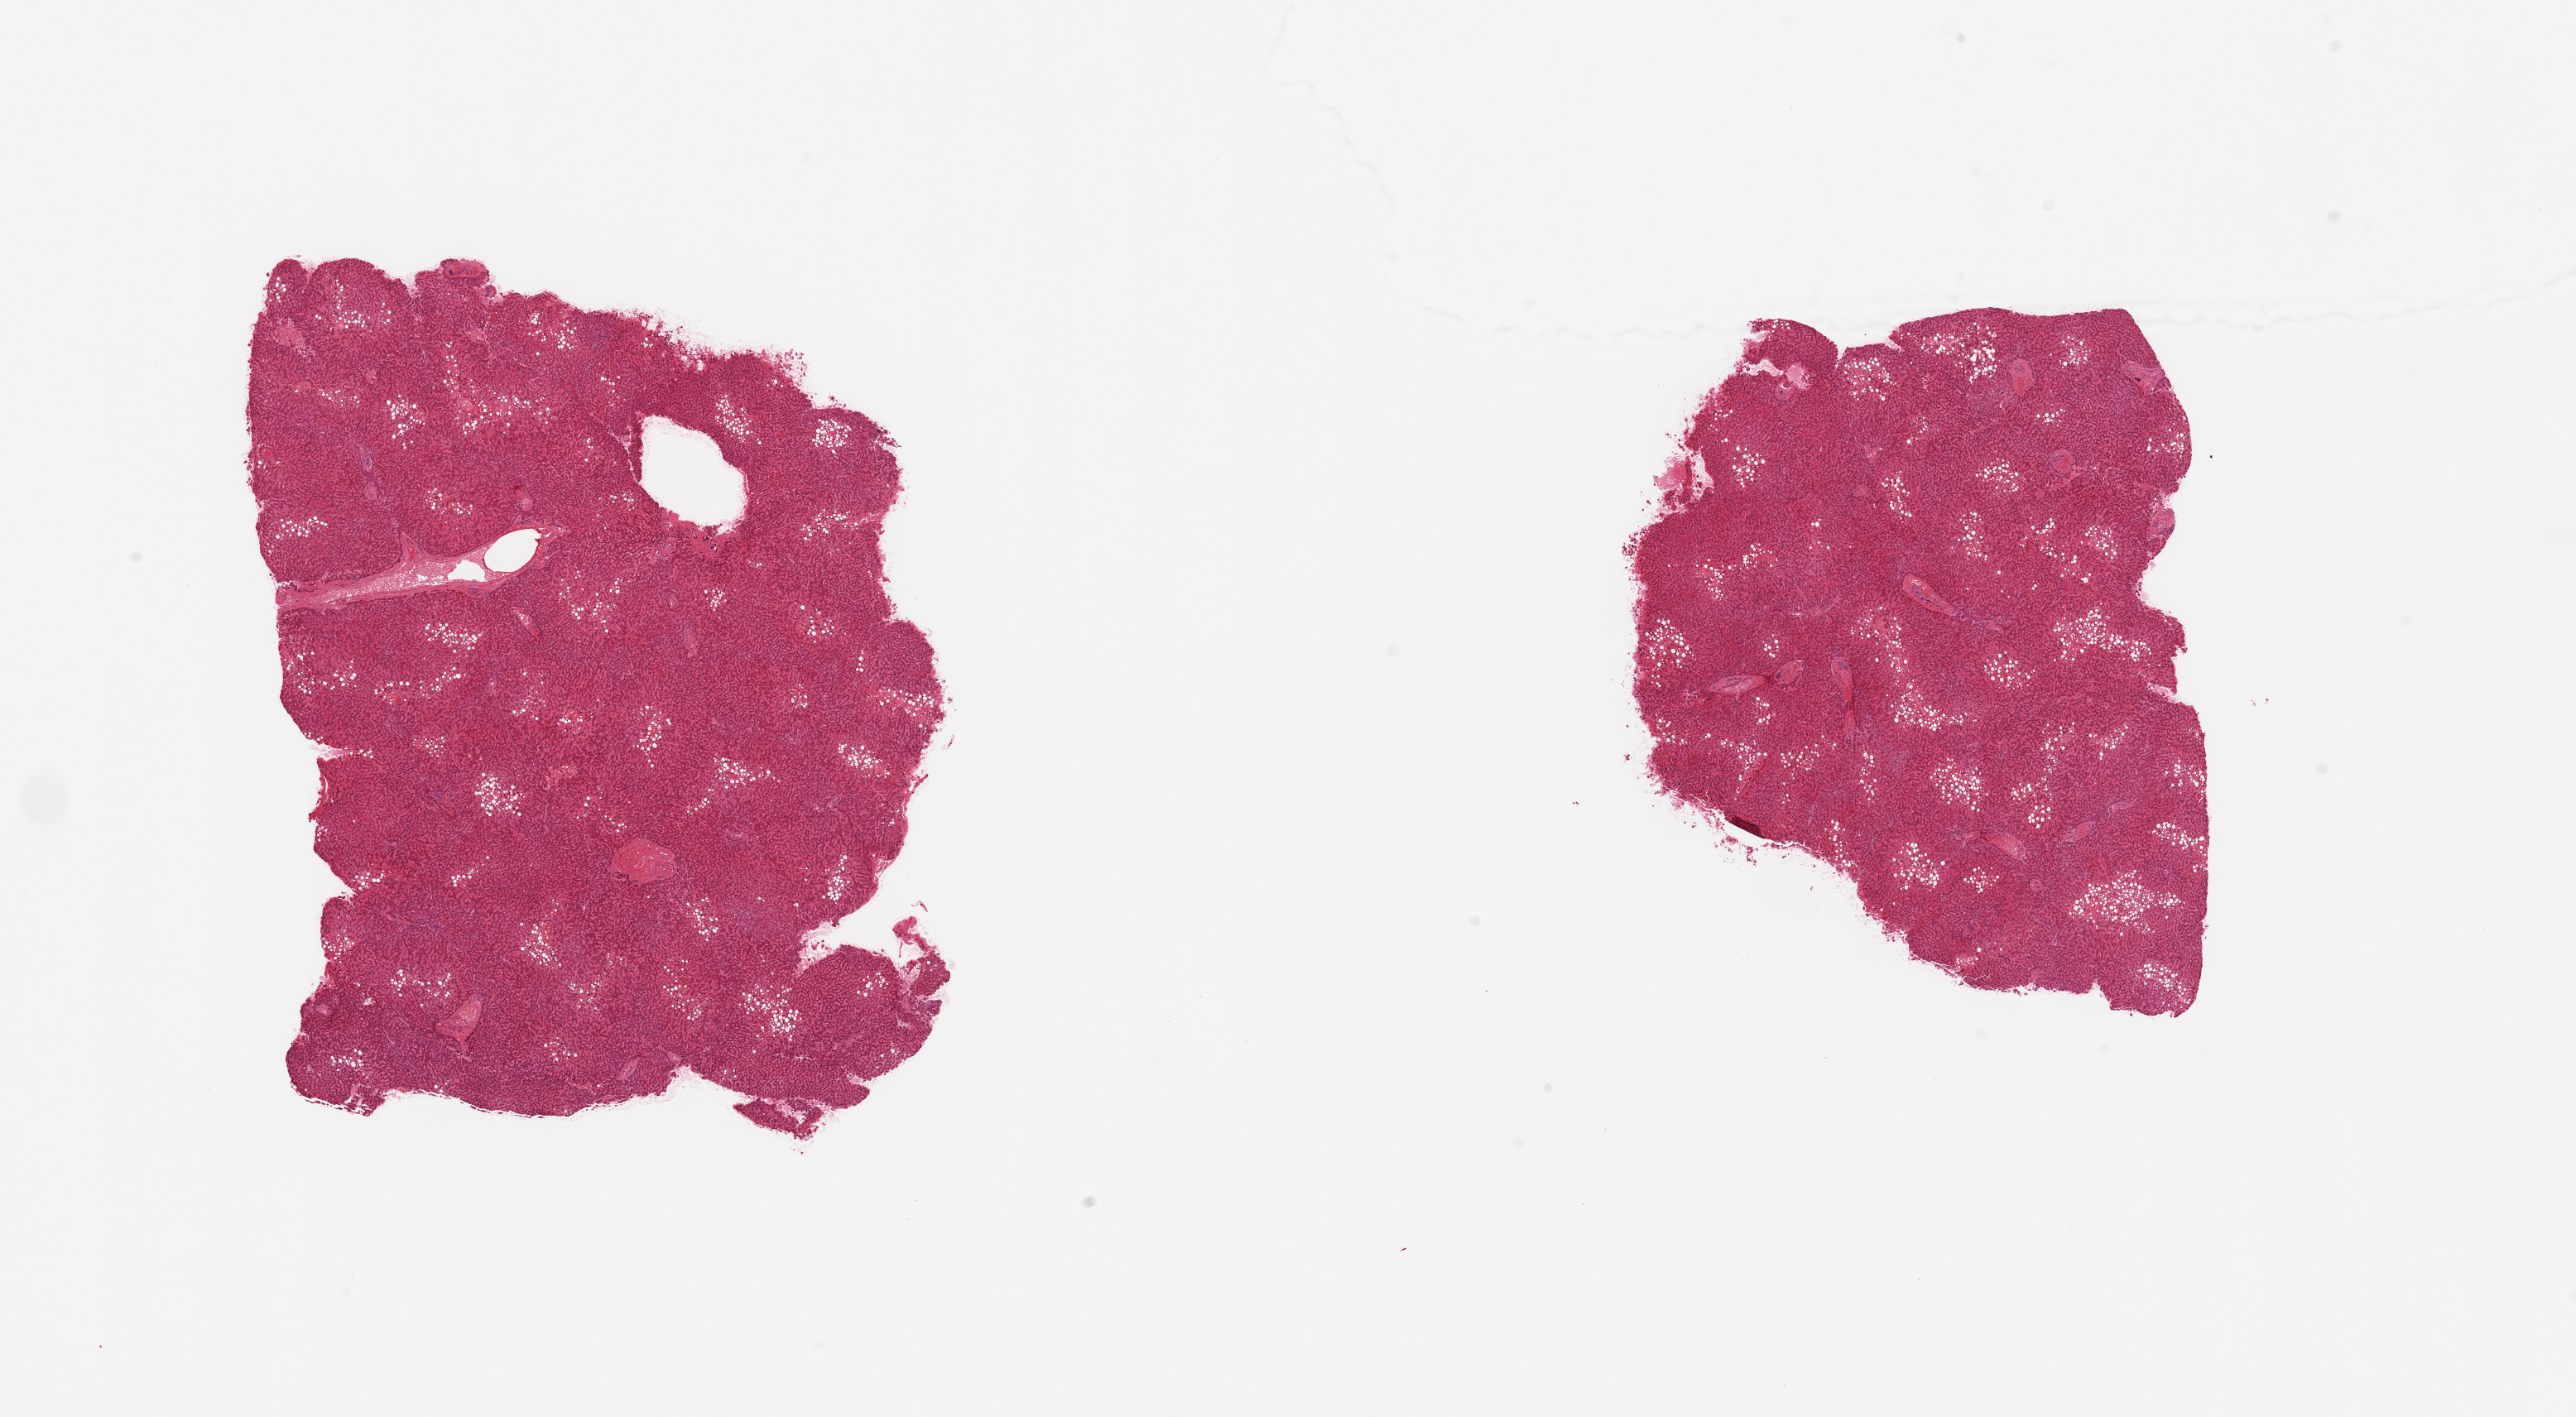
Digitized H&E-stained section, shown as a low-resolution overview of the whole scanned area (about 24.6 x 13.5 mm, from a 20x scan); PAXgene-fixed paraffin-embedded (PFPE) section; section of liver (target tissue); tissue donor sample.
* reviewer comment on this tissue sample: 2 pieces; 20% macrovesicular steatosis